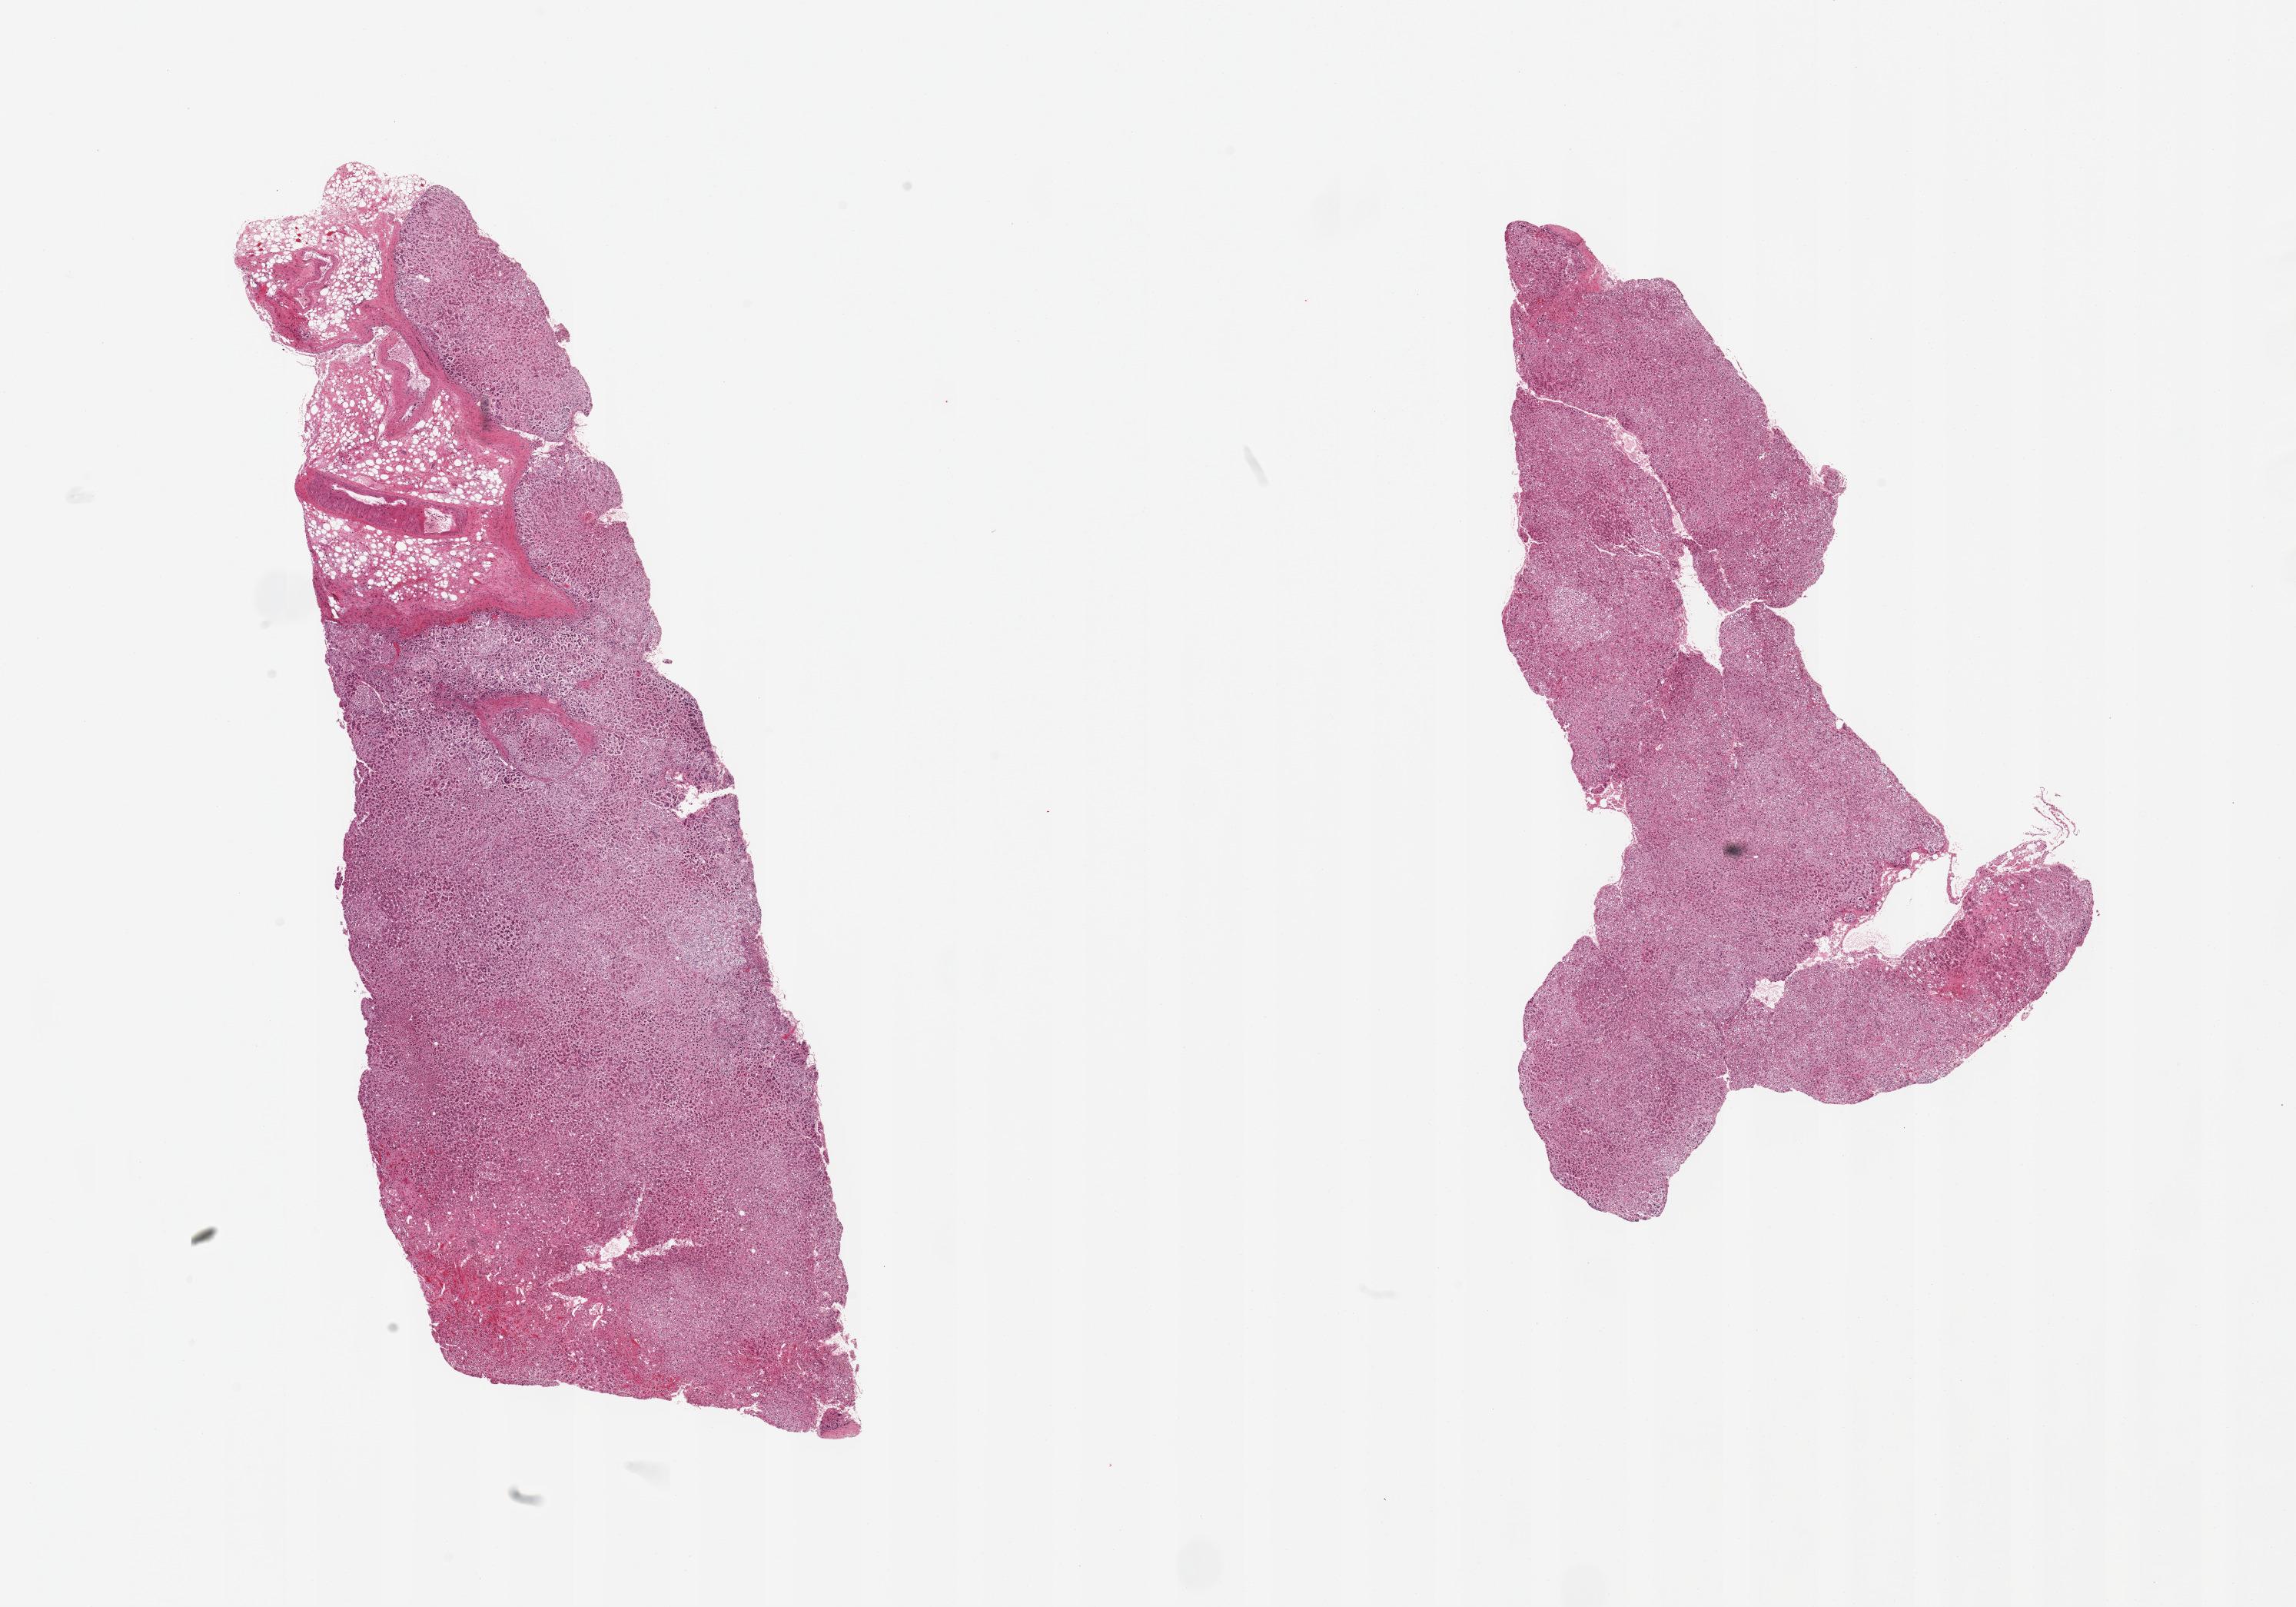
Digitized haematoxylin and eosin-stained section, brightfield — whole scanned area (about 23.6 x 16.5 mm) shown as a low-resolution overview; PAXgene-fixed, paraffin-embedded tissue; section of adrenal gland (target tissue); tissue donor sample. Donor: male.
- review note (as recorded): 2 pieces; 1 with 20% fat